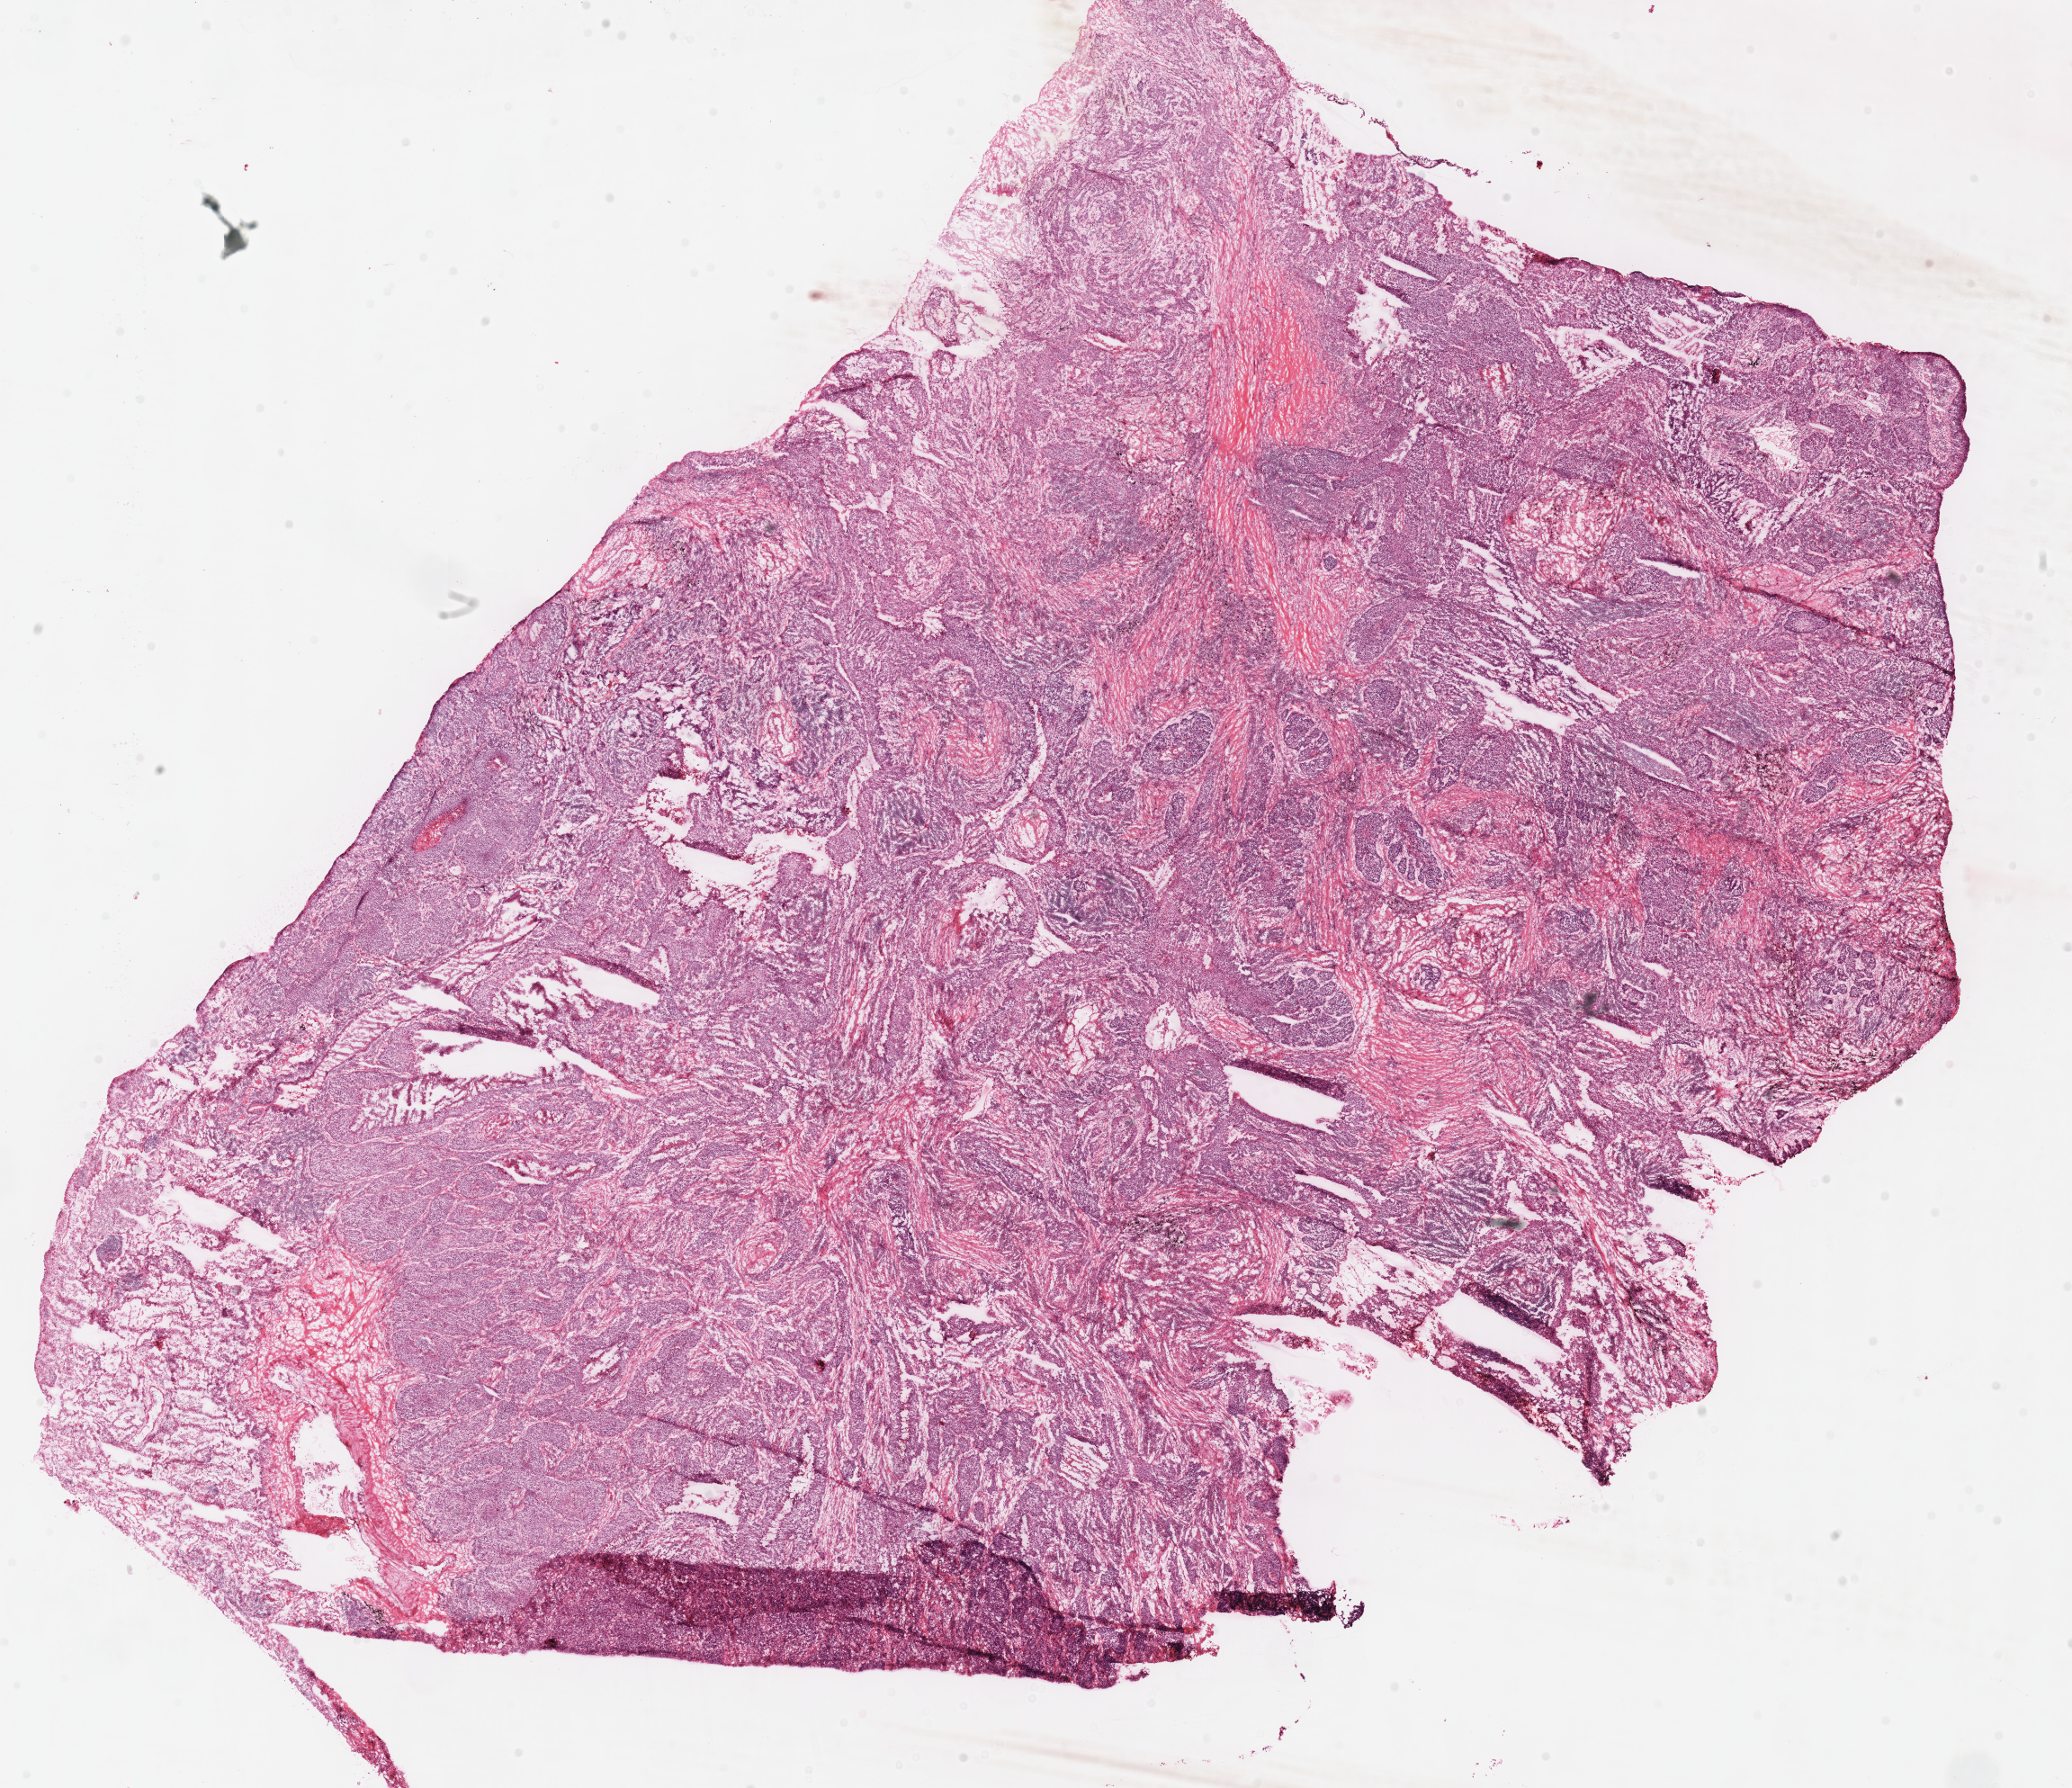
Whole-slide histology image, H&E, low-resolution overview of the scanned area, about 18.1 x 15.6 mm; frozen section from the top of the tissue portion; primary tumour sample from the lung. Patient: male, age at initial diagnosis 72 years. Pathologist review of this section (percent, as recorded): tumour cells 75%, tumour nuclei 70%, normal cells 5%, stromal cells 15%, necrosis 5%.
- laterality: left
- AJCC pathologic stage: IA (7th edition)
- histologic diagnosis: Squamous cell carcinoma, NOS (upper lobe, lung)
- TNM: T1b N0 M0